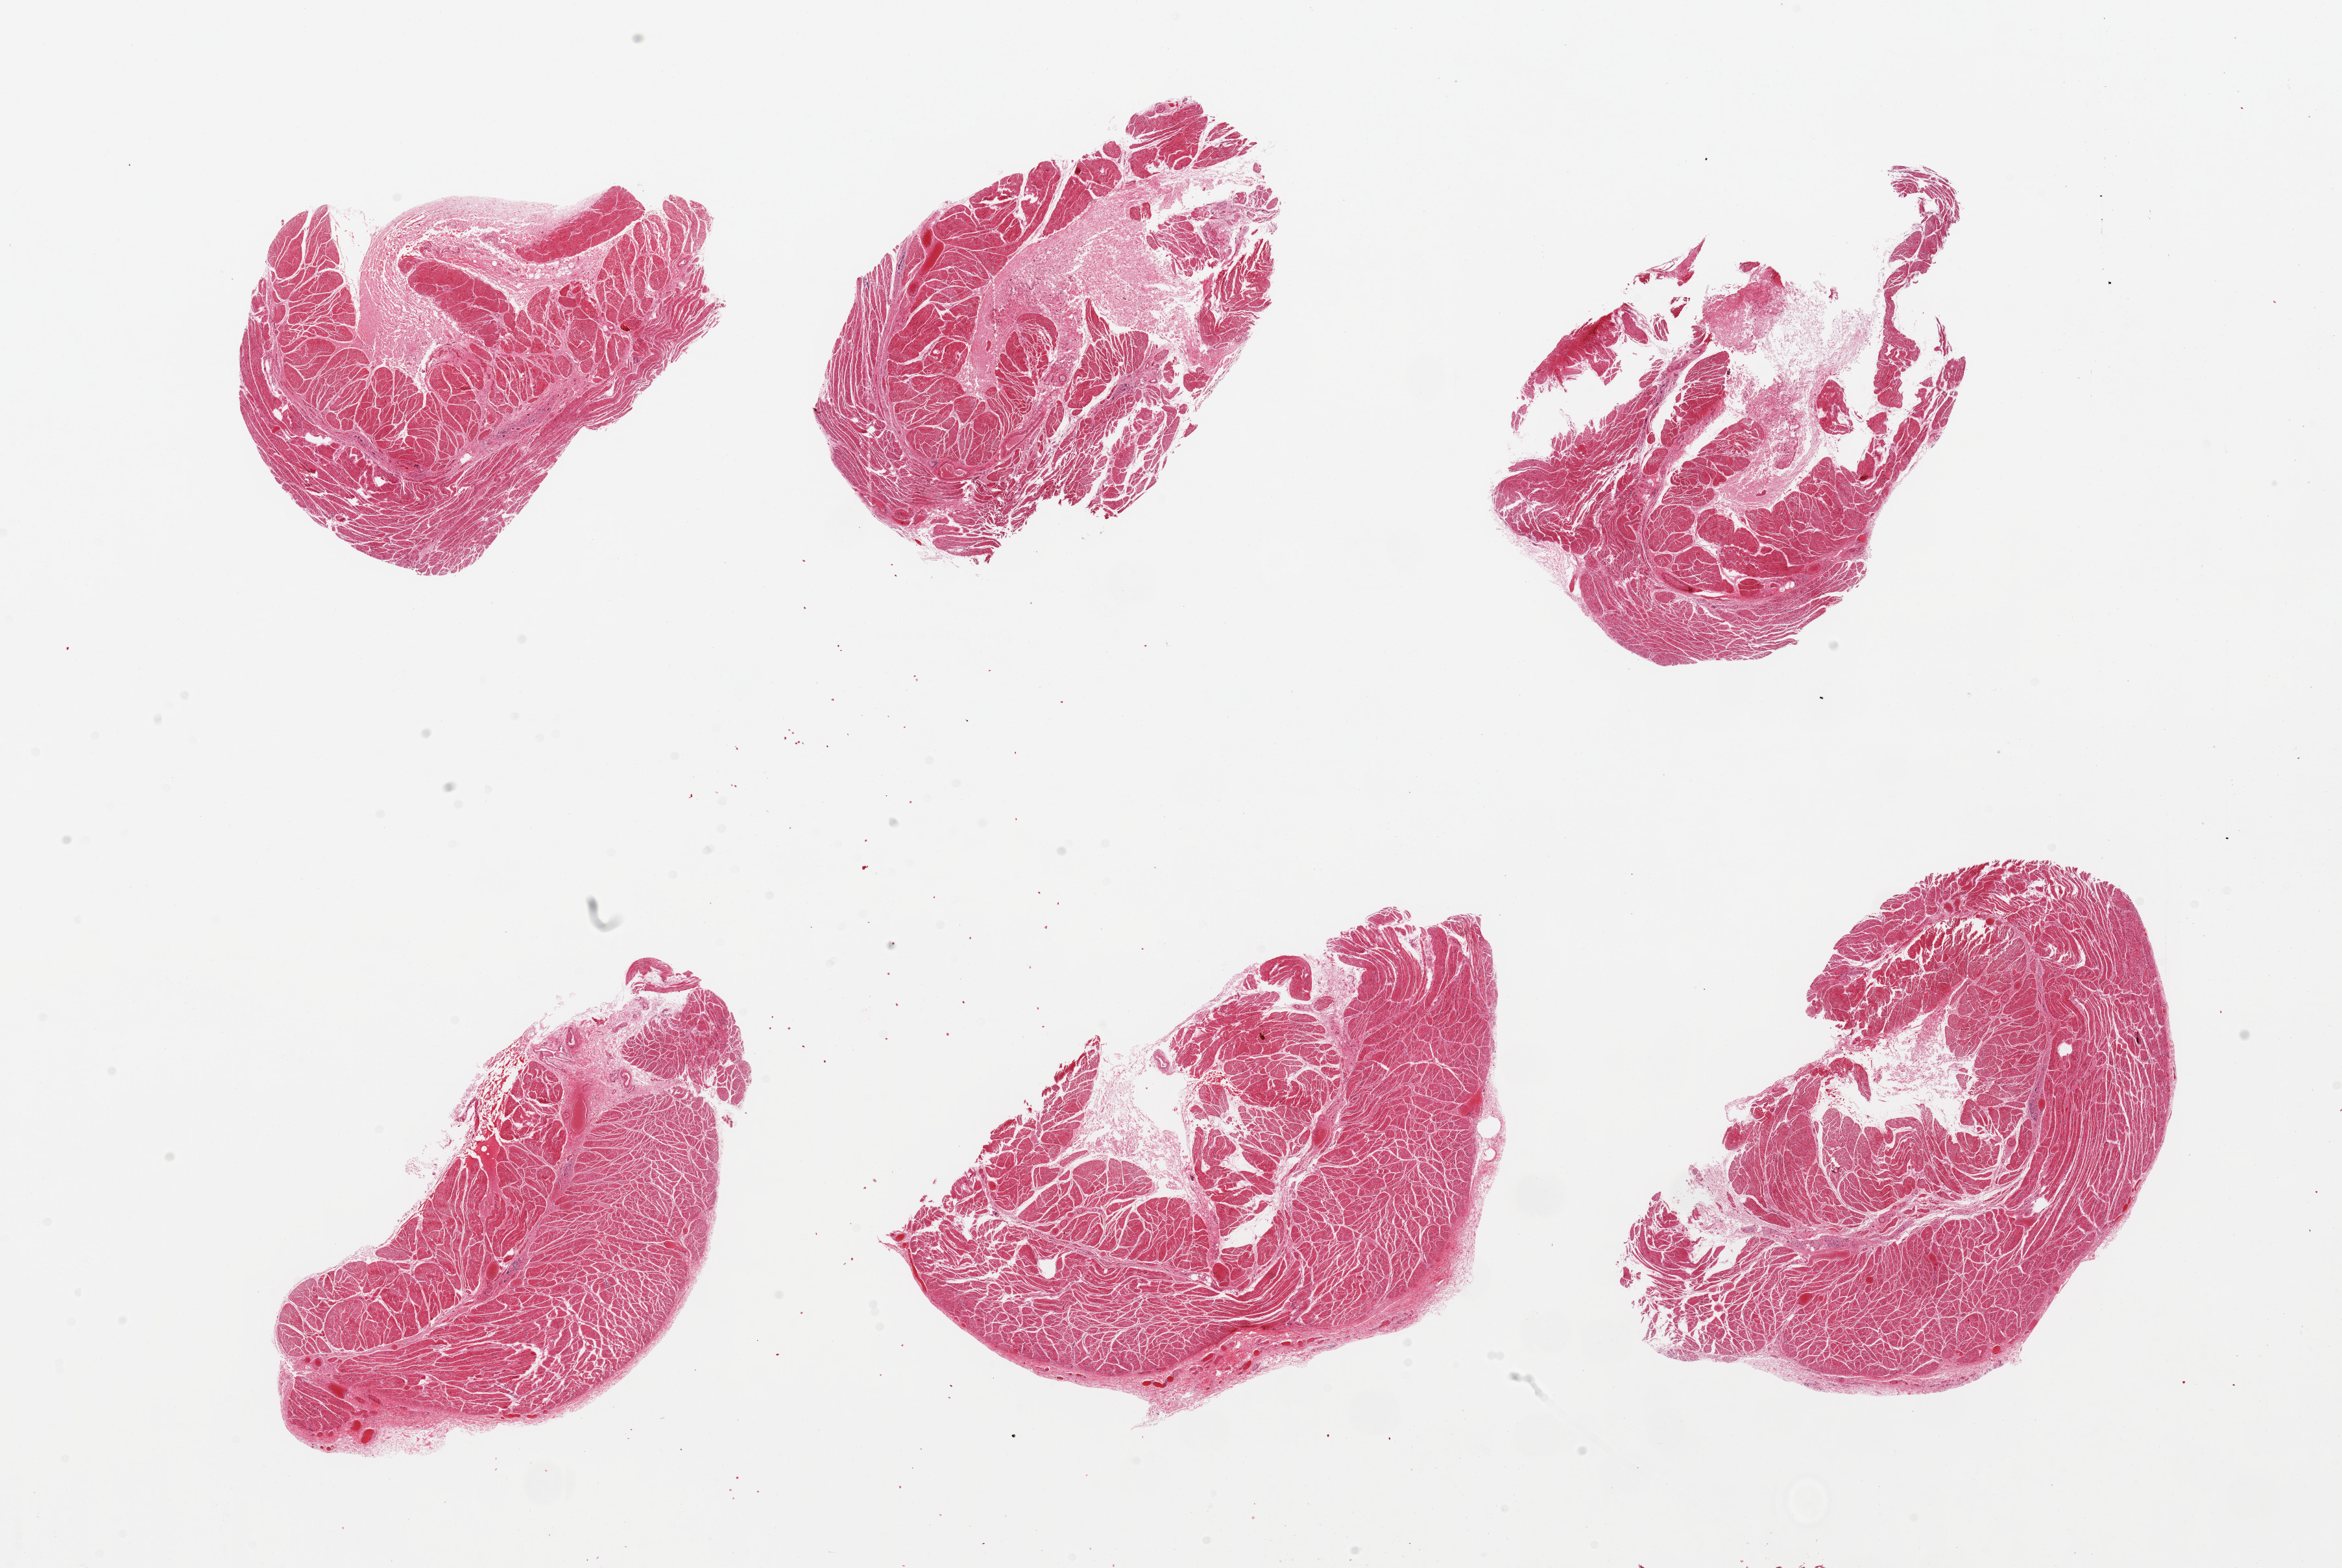
Whole-slide image, haematoxylin and eosin stain, brightfield — whole scanned area (about 28.5 x 19.1 mm) shown as a low-resolution overview, PAXgene-fixed paraffin-embedded (PFPE) section, target tissue: esophageal muscle, donor tissue sample. Donor sex: male.
Pathologist's review note for this sample: 6 pieces; 3 with 20% submucosal stroma.